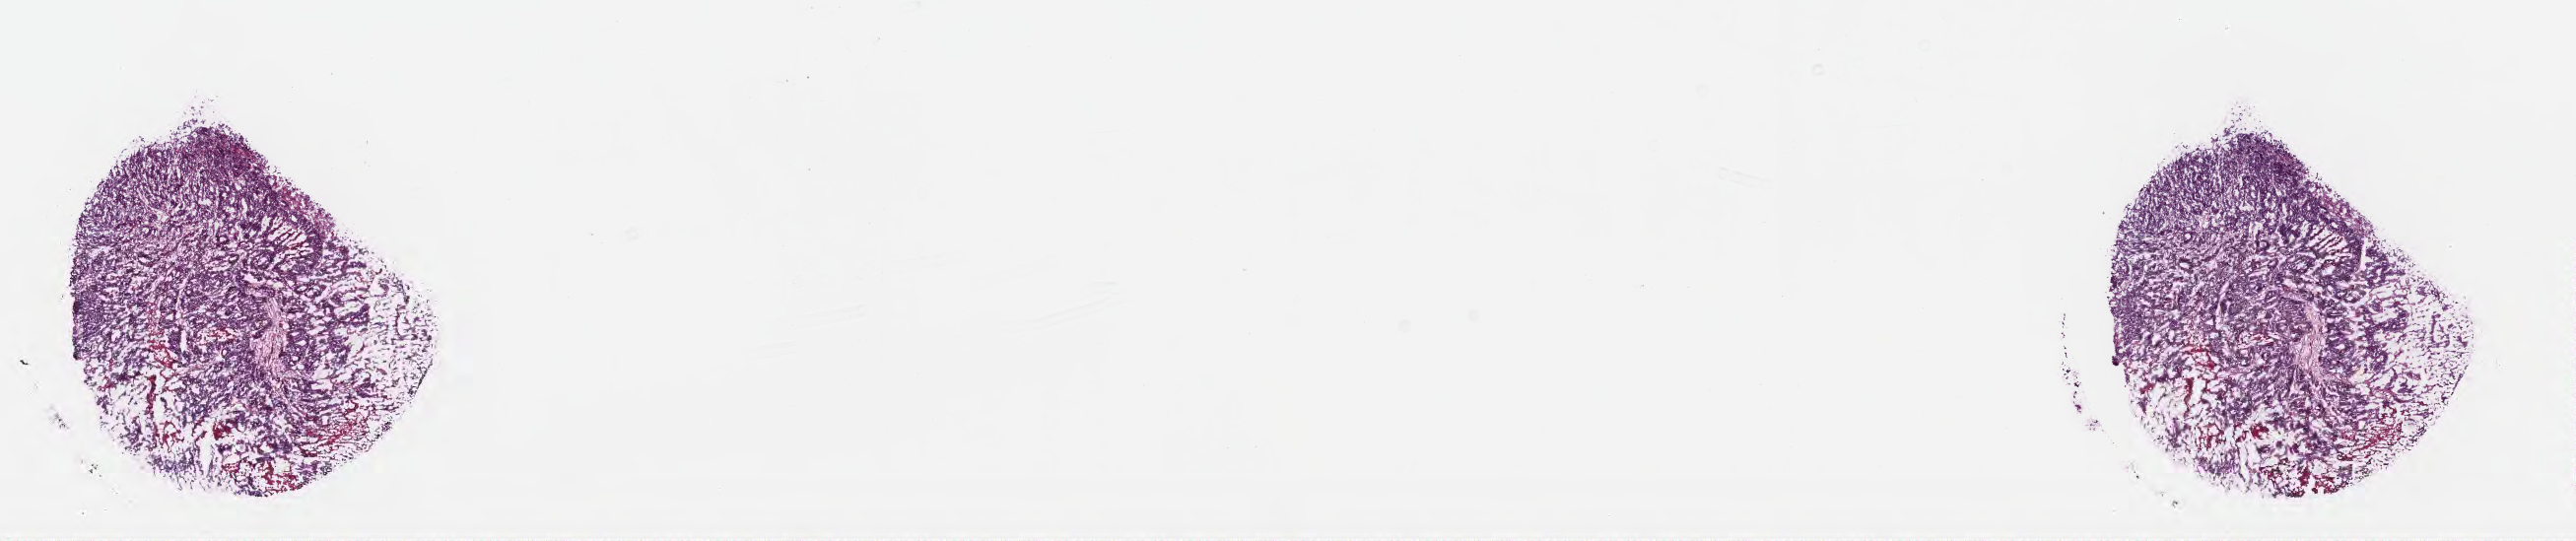
H&E whole-slide image — low-resolution overview of the scanned area, about 21.1 x 4.4 mm, frozen section (tissue freezing medium), specimen: metastatic tumor tissue, resected from liver. Male, age 46 years at initial diagnosis. Composition of this section per pathologist review: tumor cells 80%, tumor nuclei 90%, stromal cells 8%, necrosis 10%, normal cells 2%. Infiltration values recorded for this section: lymphocyte infiltration 2%, monocyte infiltration 0%, neutrophil infiltration 0%.
Section: bottom of the tissue portion. Patient diagnosis (primary): Adenocarcinoma, NOS.